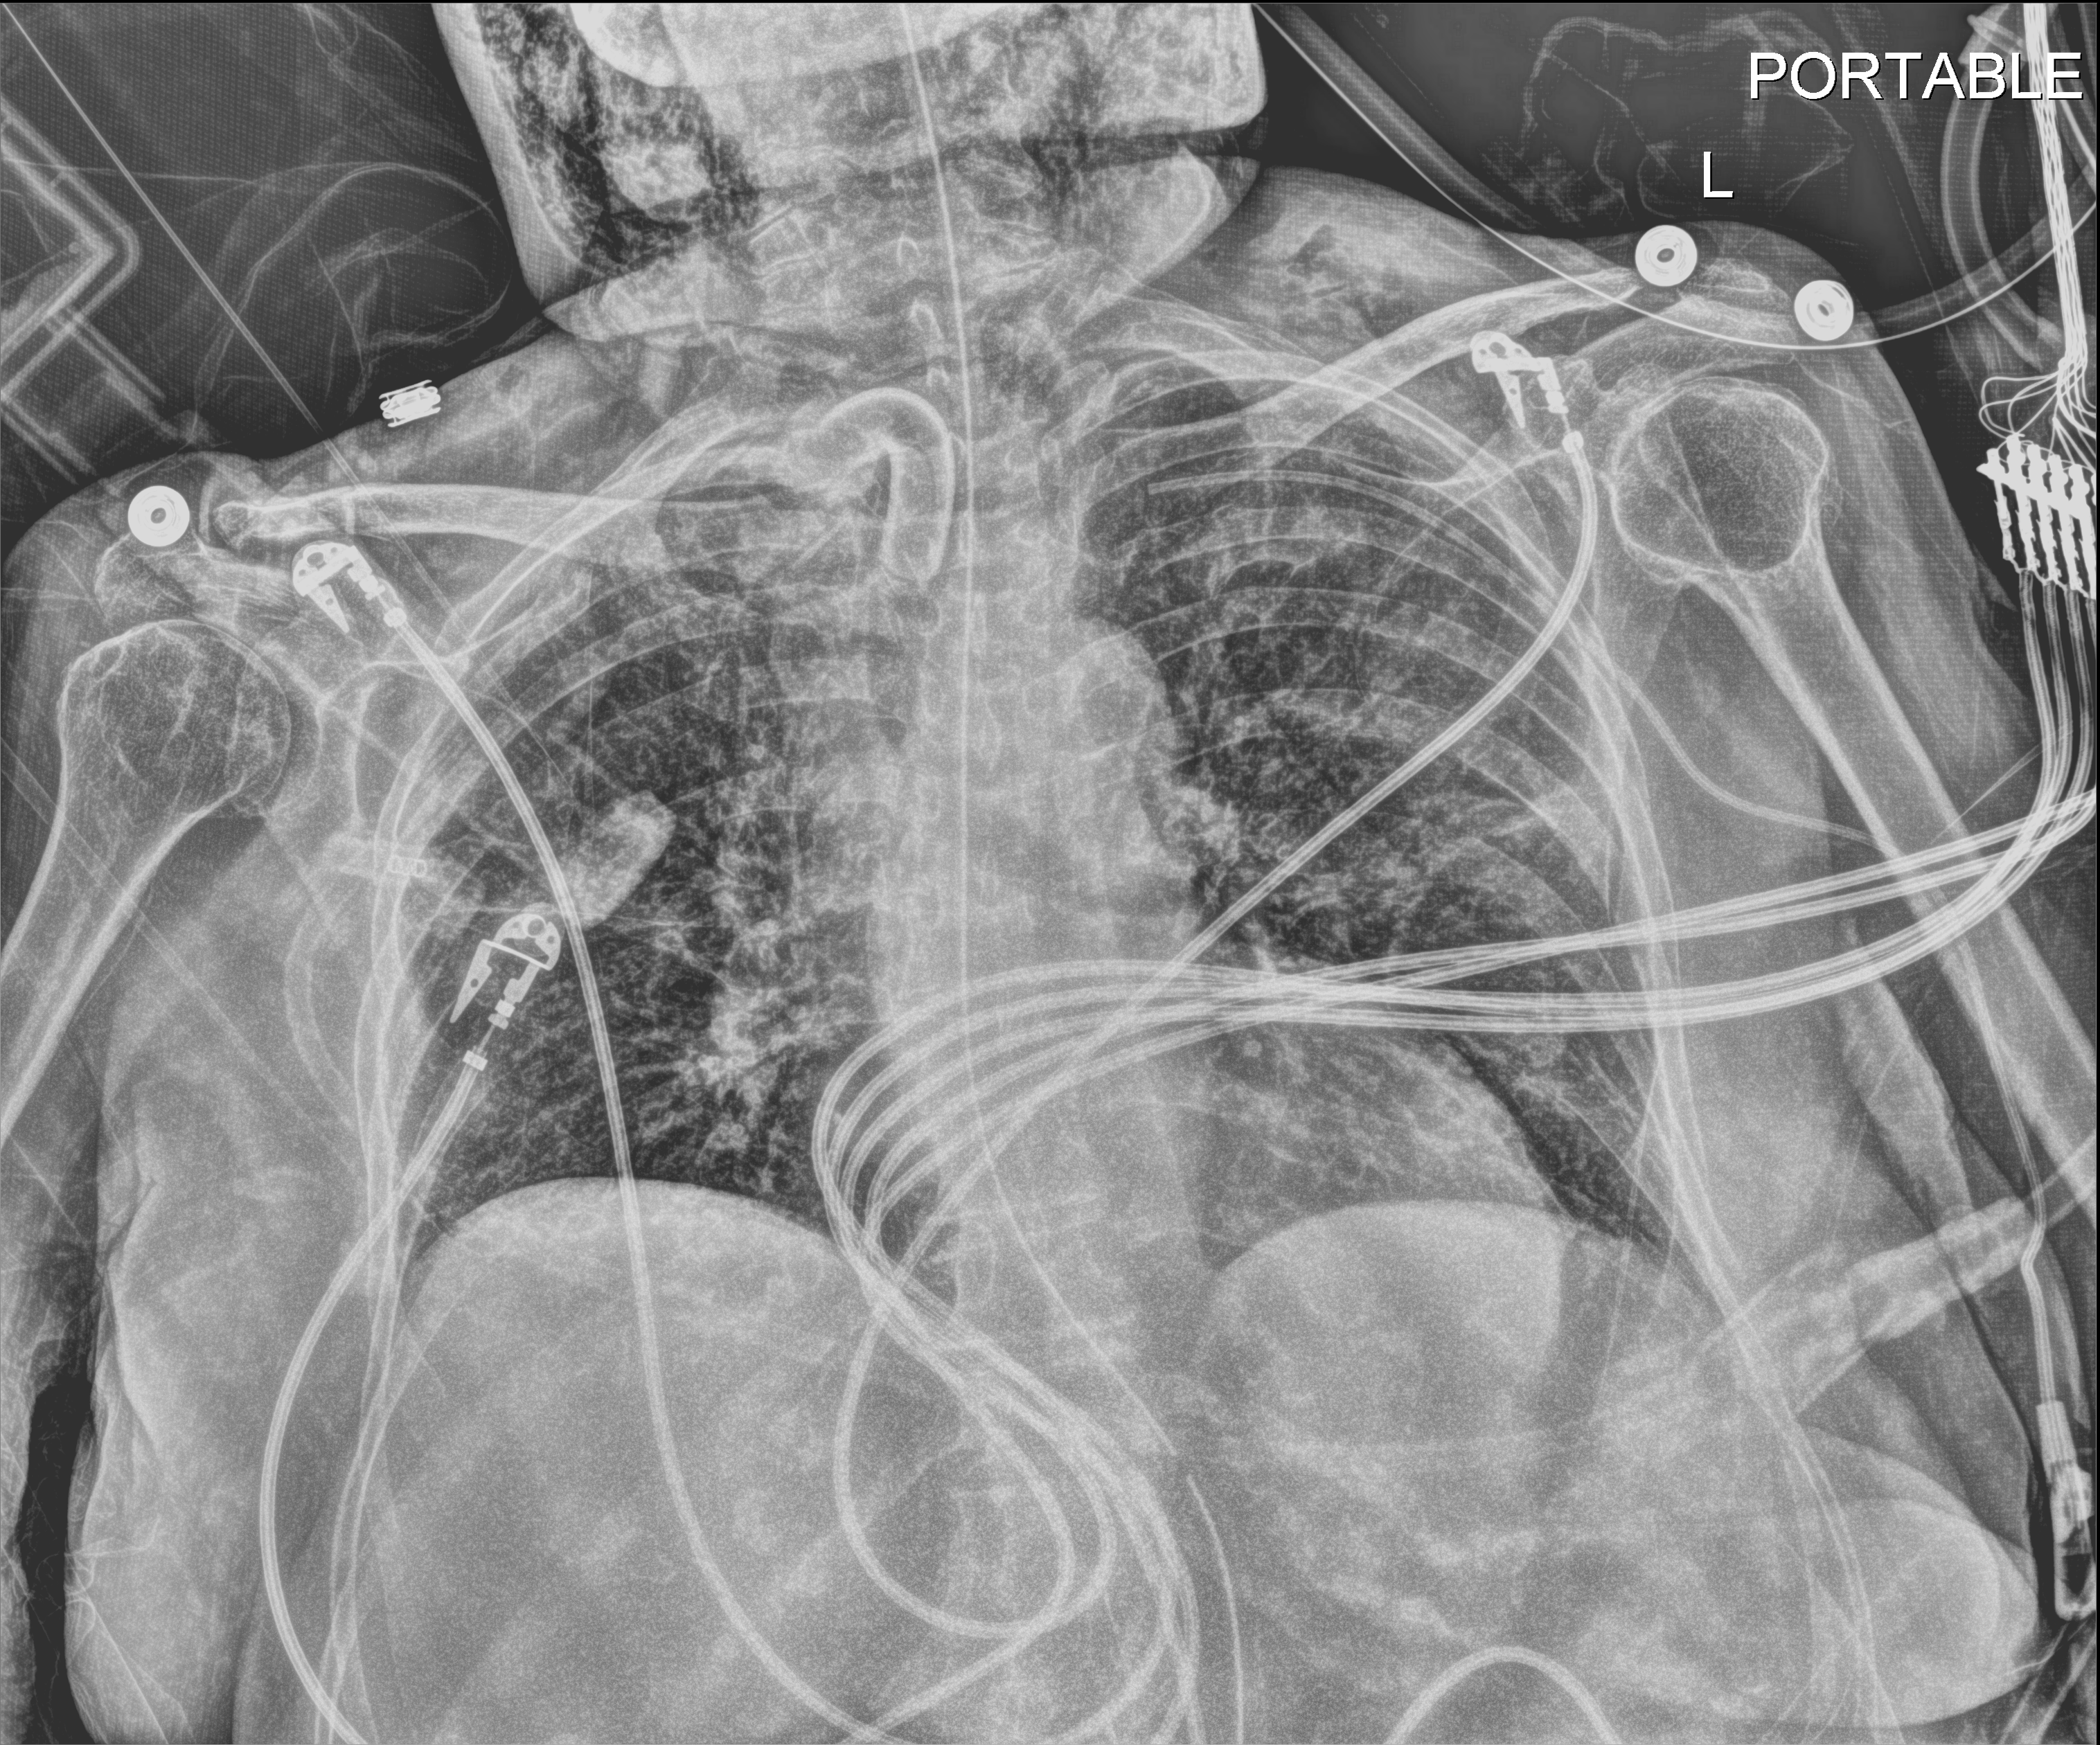
Bedside chest radiograph (digital radiography); anteroposterior (AP) projection. Patient hospitalised with COVID-19; female, aged 75–90 years.
From the hospital-stay record, not from the radiograph (when in the stay this image was taken is not recorded): mechanically ventilated during this hospital stay: yes.